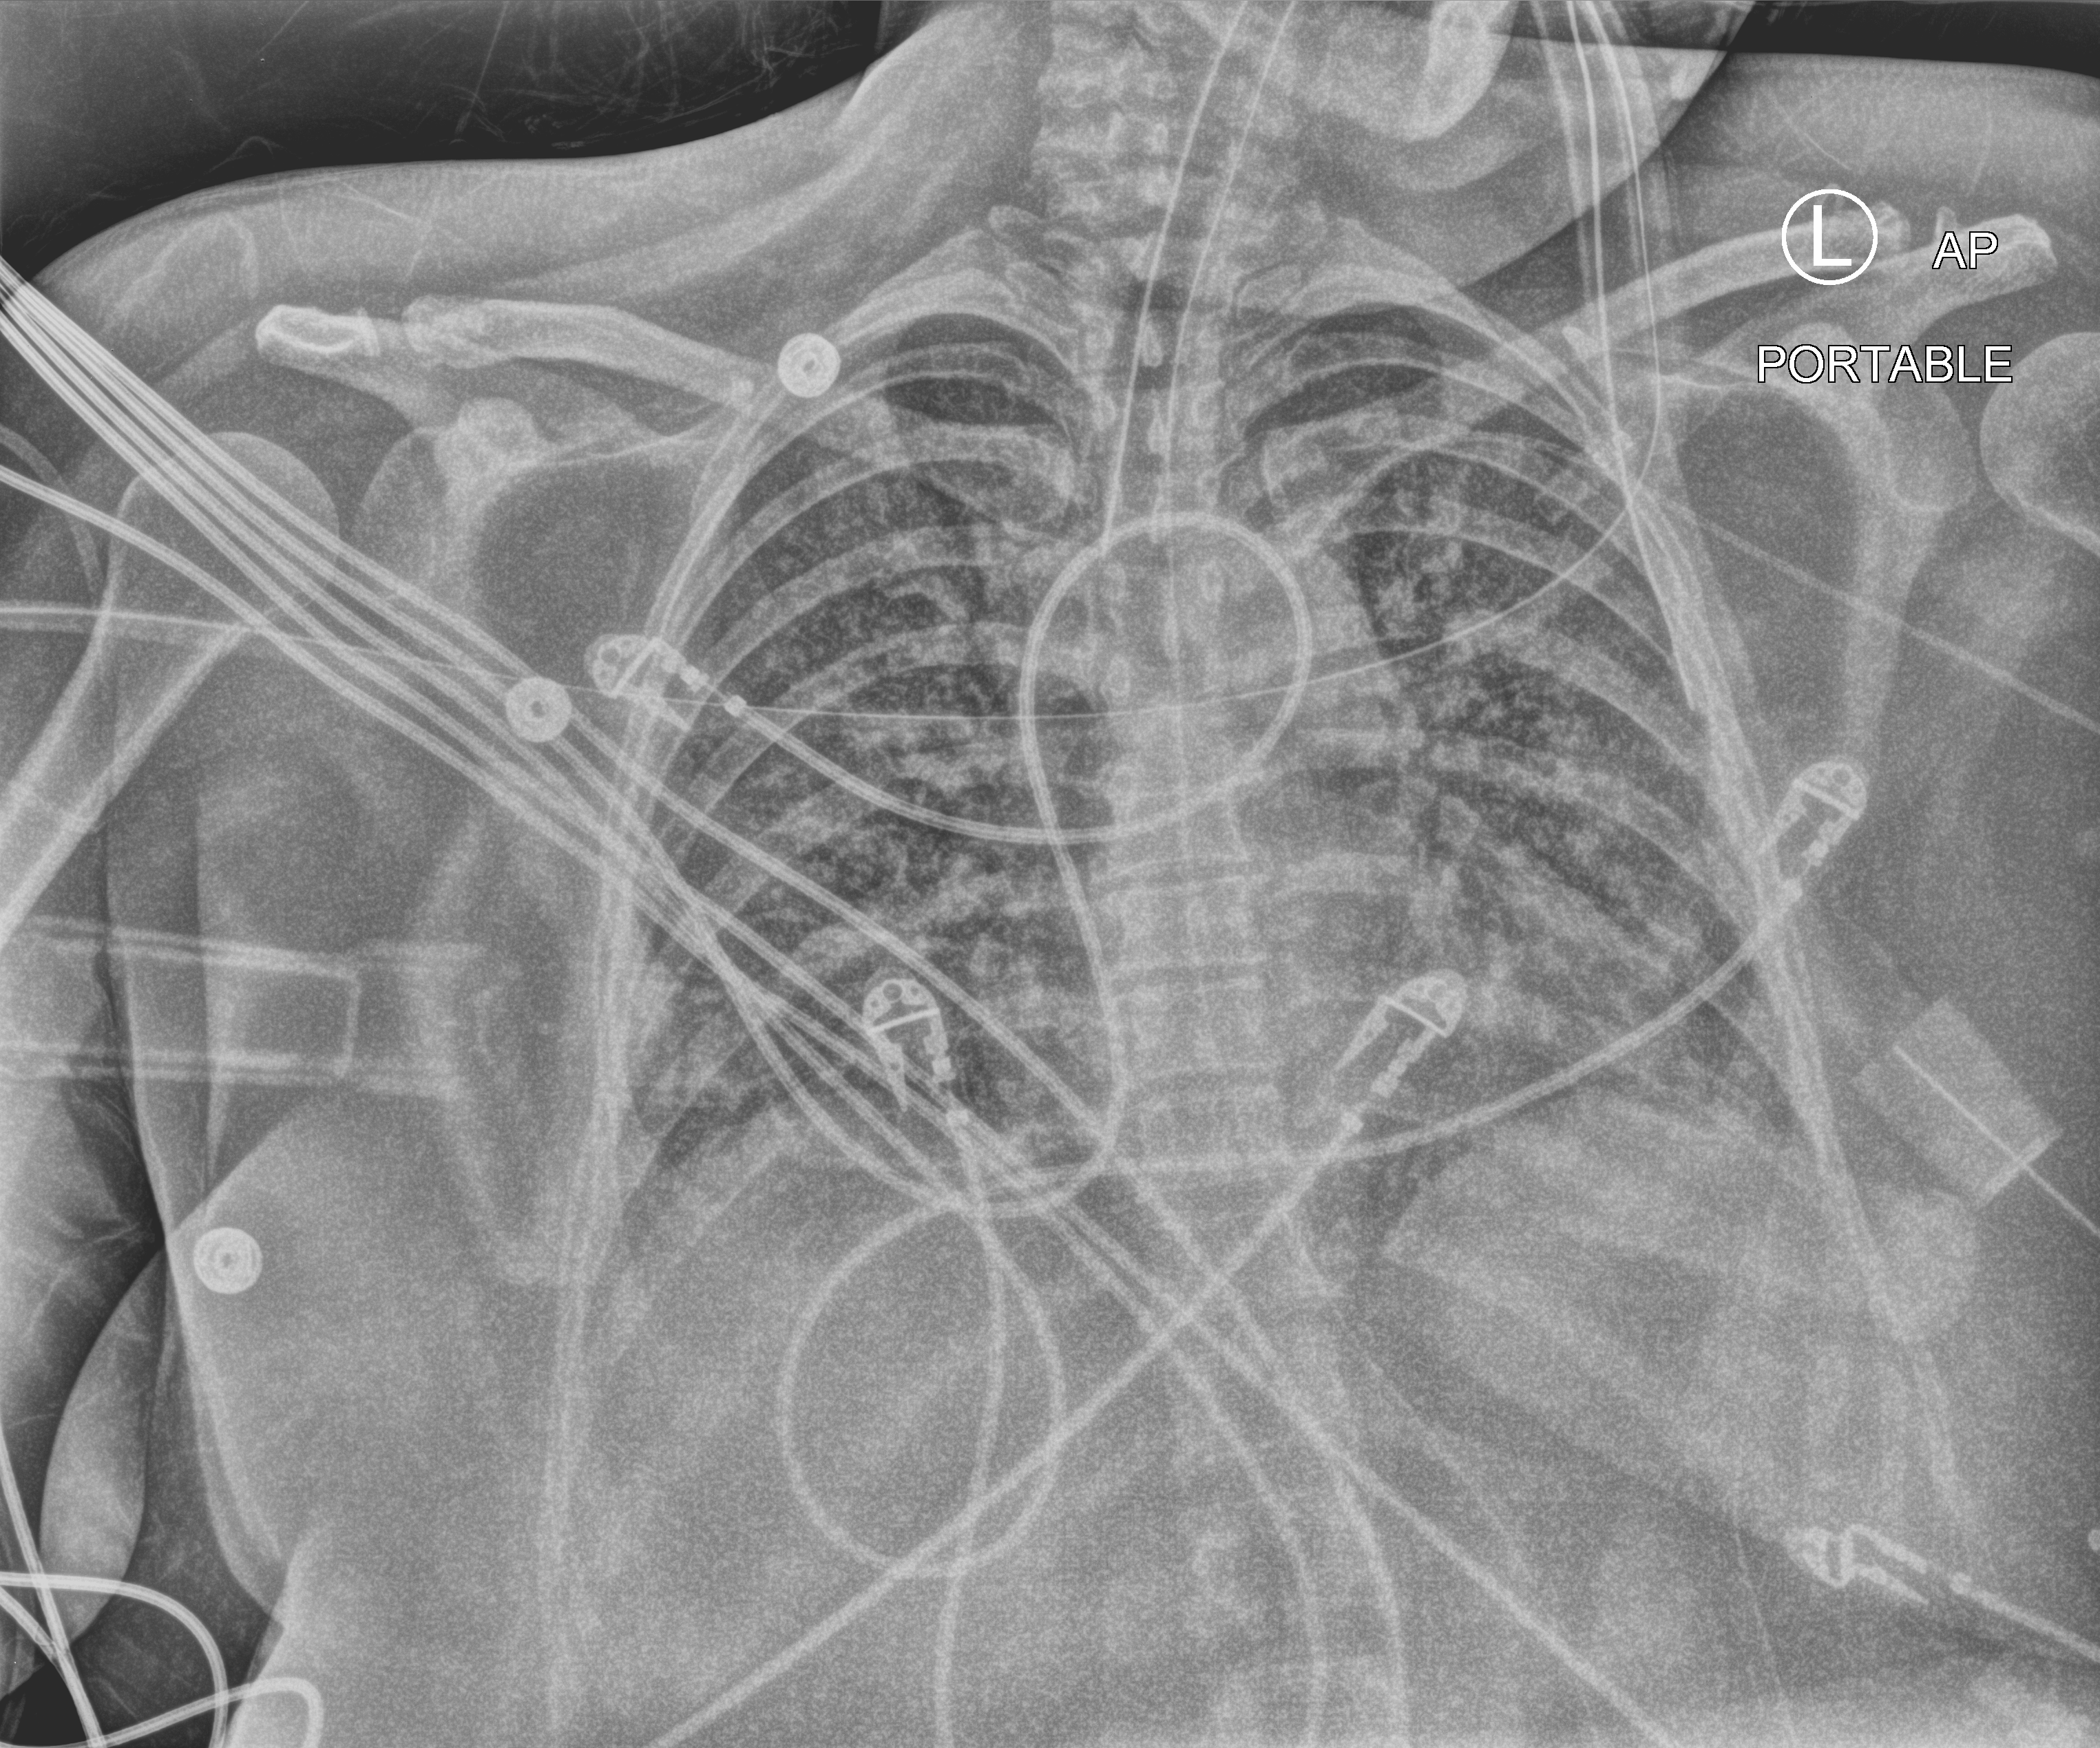
Chest X-ray (portable). Patient hospitalised with COVID-19; female, aged 18–59 years.
From the hospital-stay record, not from the radiograph (when in the stay this image was taken is not recorded): admitted to intensive care during this hospital stay: yes; diabetes (admission record): no.